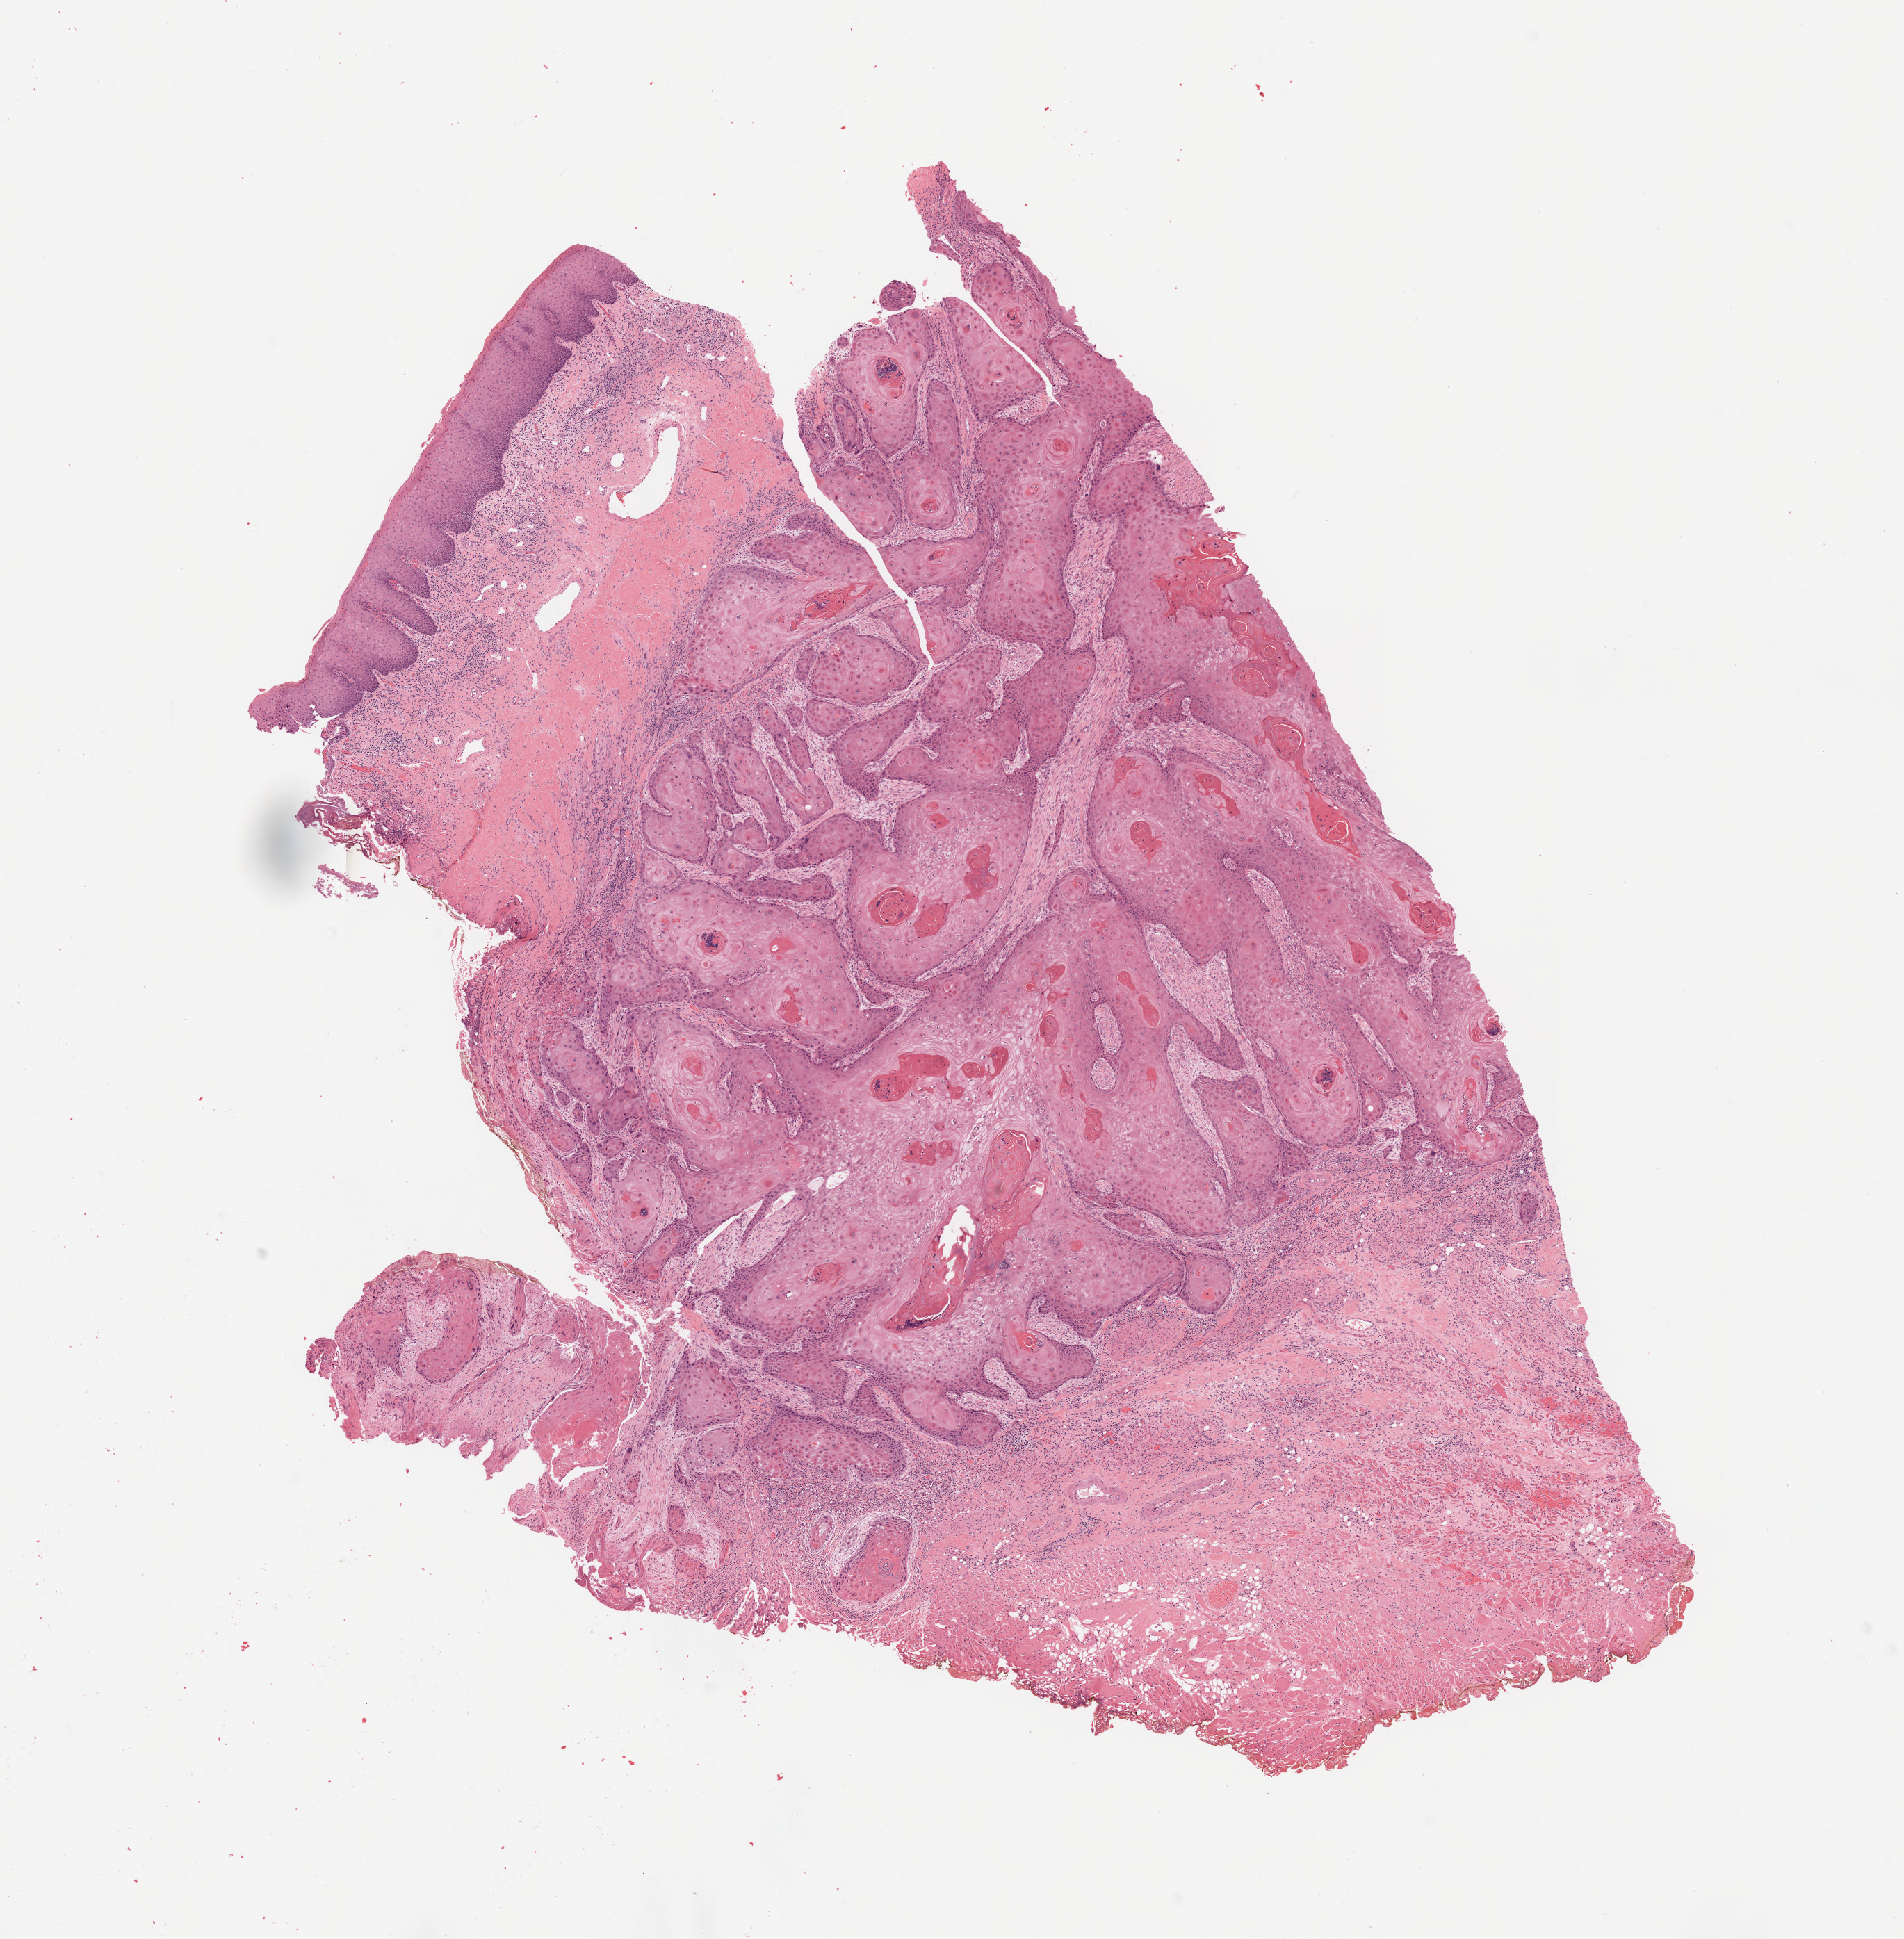
H&E-stained whole-slide image, a low-resolution overview of the entire scanned area, about 11.0 x 11.2 mm (acquisition: 20x scan). Formalin-fixed paraffin-embedded (FFPE) diagnostic section. Primary tumour sample from the head and neck. Female patient; age at initial diagnosis 76 years. Histologic grade: G2 (moderately differentiated).
AJCC pathologic stage: II (7th edition). Lymph nodes positive (case pathology): 0 of 37 examined. Histologic diagnosis: Squamous cell carcinoma, keratinizing, NOS (tongue, NOS).